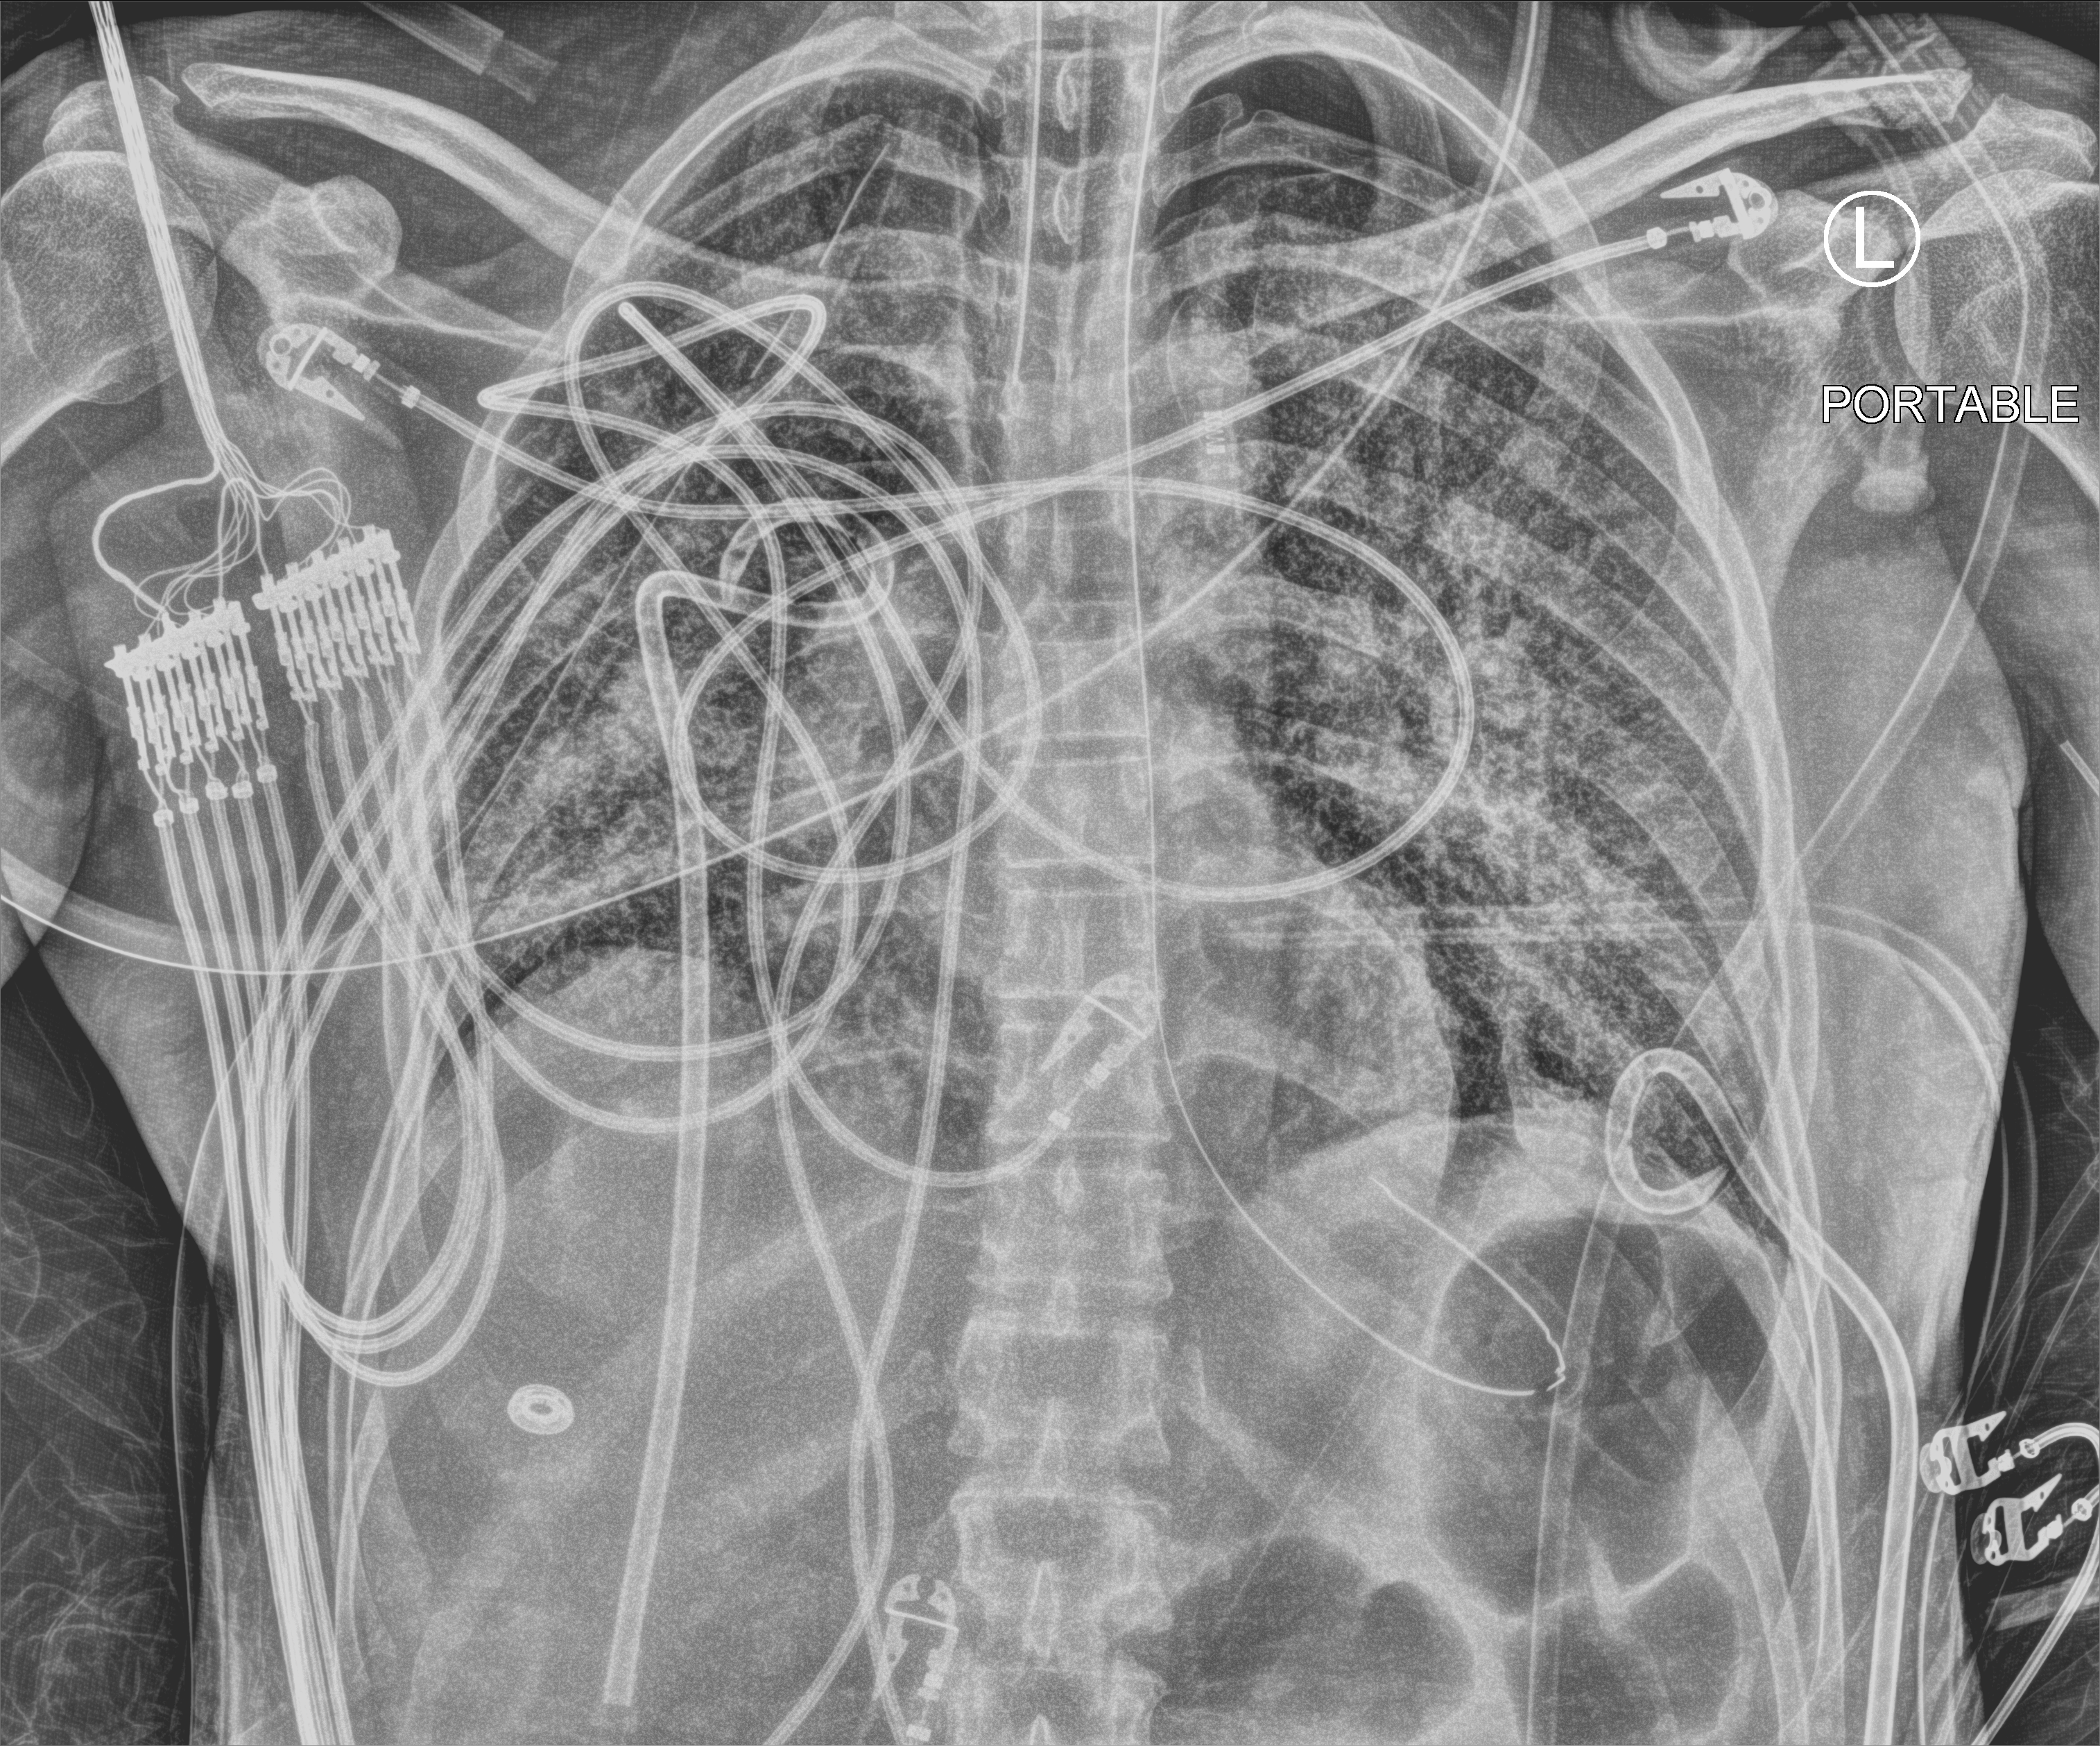
Portable chest radiograph, anteroposterior (AP) projection. Adult patient hospitalised with COVID-19, age 18–59 years.
From the hospital-stay record, not from the radiograph (when in the stay this image was taken is not recorded): other chronic lung disease (admission record): no; mechanically ventilated during this hospital stay: yes.